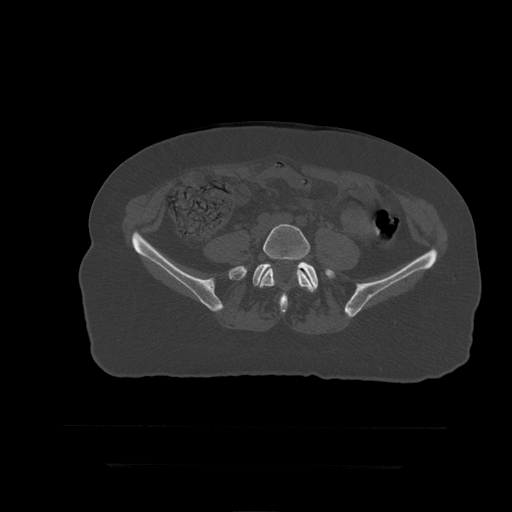
CT including the spine, one axial slice. Reconstruction kernel STANDARD. Bone window (W 1800 / L 400 HU). 512 × 512 image matrix, field of view 450 × 450 mm. Patient age 41 years. From the clinical record (not read from this slice): primary cancer: breast.
Outlined on this slice (semi-automatic segmentation, software-assisted and operator-edited):
- L5 vertebra: bounding box <260,224,316,293> (left, top, right, bottom; pixels)